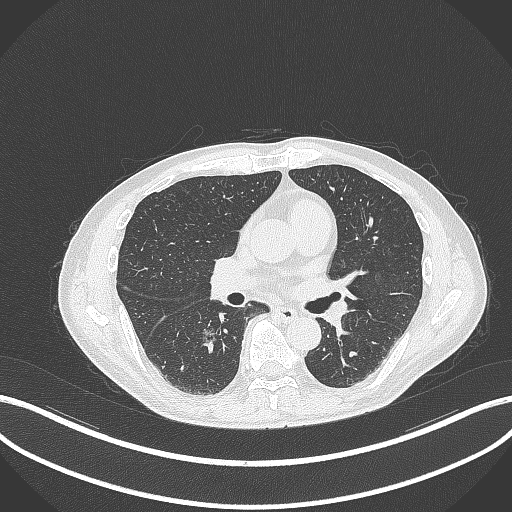
Chest CT, one axial slice; slice 171 of 323 in the series (ordered by position); 120 kVp; lung window (W 1500 / L -600 HU); 1 mm slice thickness; 512 × 512 image matrix. Male patient, age 61 years. From the clinical record (not read from this slice): clinical TNM (as recorded): T1c N0 M0.
Outlined on this slice (rectangle marked by the reading radiologist):
- lung tumour (recorded histology: adenocarcinoma): bounding box <199,321,219,350> (left, top, right, bottom; pixels)